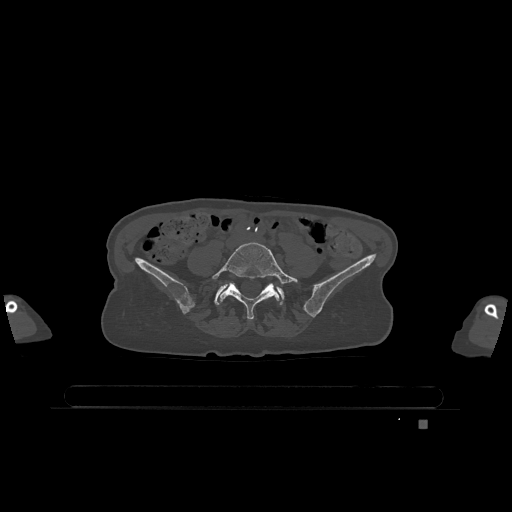
CT including the spine, one axial slice; slice 238 of 1317 in the series (ordered by position); bone window (W 1800 / L 400 HU); 512 × 512 image matrix, field of view 500 × 500 mm. Female patient, age 74 years. Case-level facts recorded for this patient, not image findings: primary cancer: lung.
Outlined on this slice (semi-automatic segmentation, software-assisted and operator-edited):
- L5 vertebra: box from (x=212, y=242) to (x=298, y=320) px